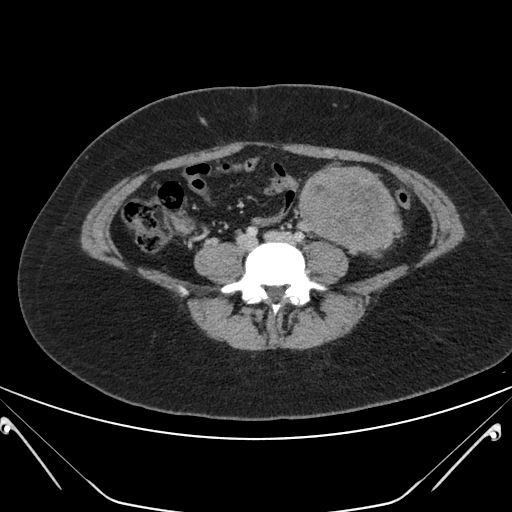
Contrast-enhanced abdominal CT, one axial slice; position 71 of 168 along the scan axis; 120 kVp; intravenous contrast given; soft-tissue window (W 400 / L 40 HU); 3 mm slice thickness; 512 × 512 image matrix, field of view 394 × 394 mm. Patient: female, 26 years. Case-level facts recorded for this patient, not image findings: diagnosis: adrenocortical carcinoma; tumour side: left adrenal; tumour size at pathology: 28 cm; Ki-67 index: 20 %; stage (as recorded): 2.
Structures marked on this image (semi-automatically segmented with operator editing):
- mass: bounding box [x1, y1, x2, y2] px = [301, 168, 396, 252]